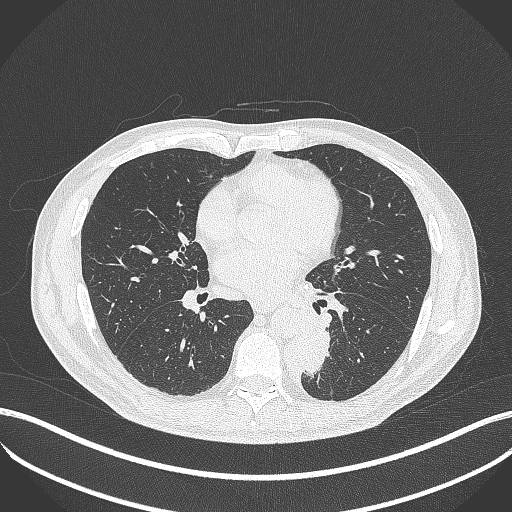
Chest CT, one axial slice. Reconstruction kernel B70f. Lung window (W 1500 / L -600 HU). 1 mm slice thickness. 512 × 512 image matrix, field of view 400 × 400 mm. Patient: male, 72 years. From the clinical record (not read from this slice): clinical TNM (as recorded): T2b N0 M1.
Outlined on this slice (rectangle marked by the reading radiologist):
- lung tumour (recorded histology: adenocarcinoma): bounding box [x1, y1, x2, y2] px = [303, 325, 337, 378]